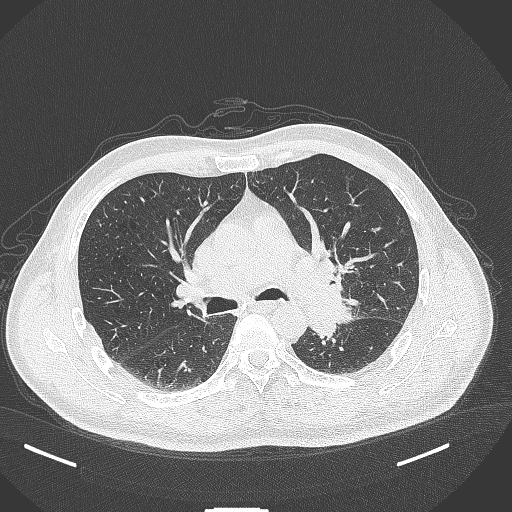
Chest CT, one axial slice. Position 253 of 429 along the scan axis. 120 kVp. Lung window (W 1500 / L -600 HU). 512 × 512 image matrix, field of view 400 × 400 mm. Patient: male, 55 years. From the clinical record (not read from this slice): clinical TNM (as recorded): T3 N0 M1c.
Outlined on this slice (rectangle marked by the reading radiologist):
- lung tumour (recorded histology: adenocarcinoma): bounding box (x1, y1, x2, y2) in pixels: (299, 288, 363, 343)